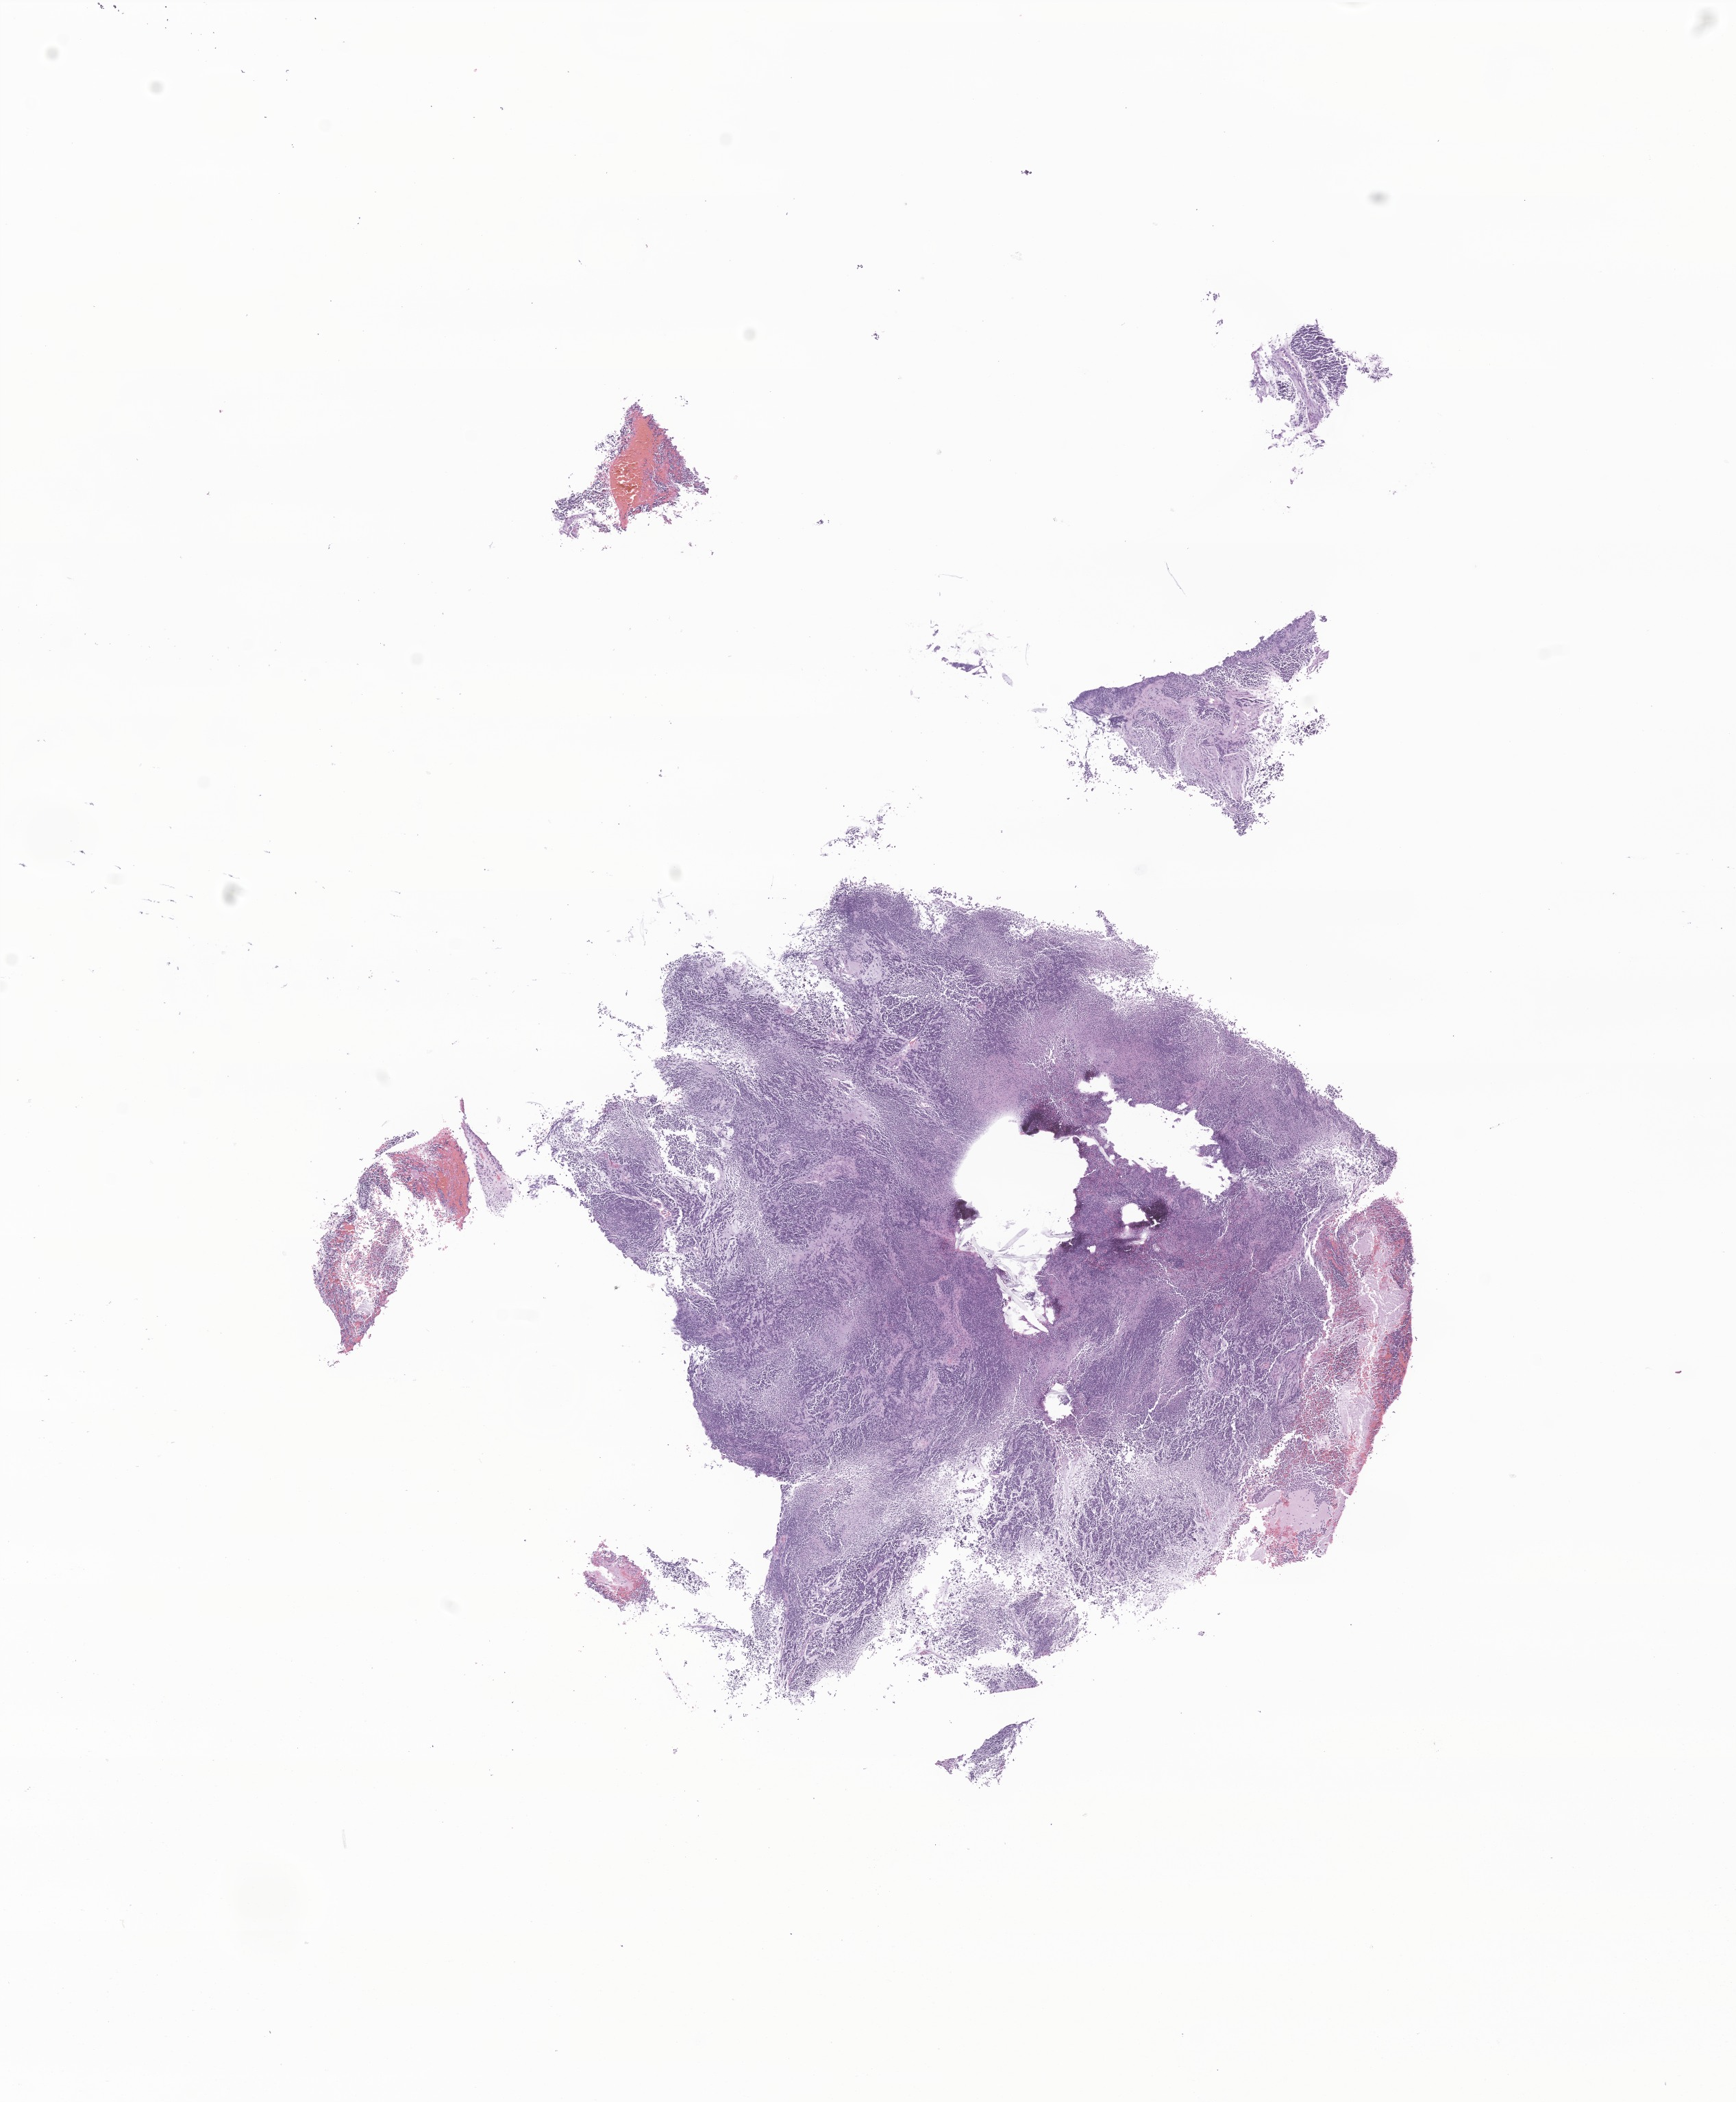
Whole-slide image, haematoxylin and eosin stain of tumor tissue from the brain — shown as a low-resolution overview of the whole scanned area (about 10.7 x 12.9 mm); formalin-fixed, paraffin-embedded (FFPE) tissue. Patient male; age 146 months (12 years 2 months).
Diagnosis (ICD-O-3 morphology term): Large cell medulloblastoma.